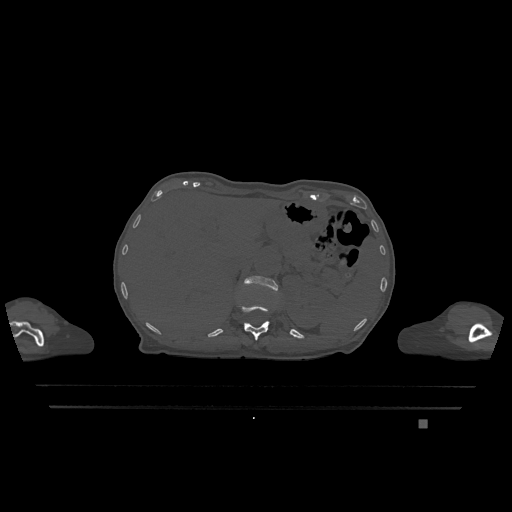
CT including the spine, one axial slice. Position 520 of 1317 along the scan axis. Bone window (W 1800 / L 400 HU). 512 × 512 image matrix, field of view 500 × 500 mm. Female patient, age 74 years. From the clinical record (not read from this slice): primary cancer: lung; vertebrae with lytic lesions (as recorded): T1, T4, T5, T6, L4, L5.
Outlined on this slice (semi-automatic segmentation, software-assisted and operator-edited):
- L1 vertebra: bounding box (x1, y1, x2, y2) in pixels: (244, 275, 278, 293)
- T12 vertebra: (239, 305, 270, 340)